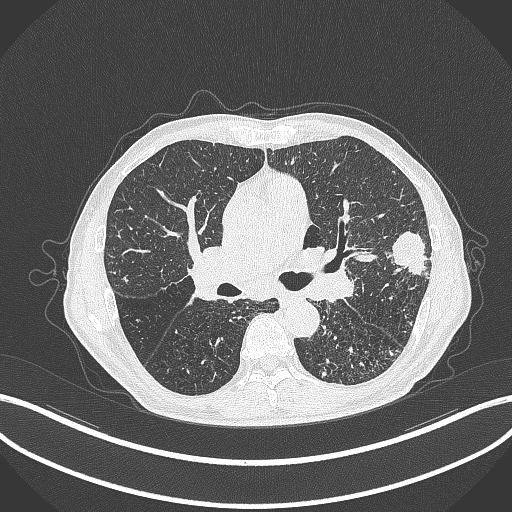
Chest CT, one axial slice. Slice 240 of 463 in the series (ordered by position). 120 kVp. Lung window (W 1500 / L -600 HU). 1 mm slice thickness. 512 × 512 image matrix, field of view 400 × 400 mm. Patient: male, 74 years. From the clinical record (not read from this slice): clinical TNM (as recorded): T2a N1 M0.
Structures marked on this image (bounding box drawn by a radiologist):
- lung tumour (recorded histology: adenocarcinoma): bounding box <387,230,430,286> (left, top, right, bottom; pixels)